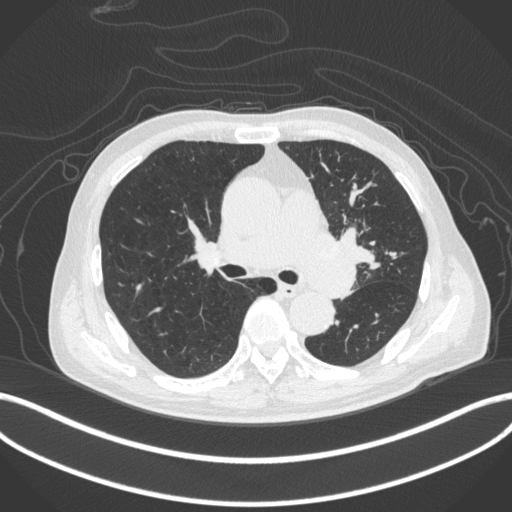
Chest CT, one axial slice. Position 263 of 420 along the scan axis. Lung window (W 1500 / L -600 HU). 1 mm slice thickness. 512 × 512 image matrix, field of view 400 × 400 mm. Patient: male, 77 years. From the clinical record (not read from this slice): clinical TNM (as recorded): T3 N1 M0.
Structures marked on this image (bounding box drawn by a radiologist):
- lung tumour (recorded histology: adenocarcinoma): bounding box (x1, y1, x2, y2) in pixels: (300, 228, 368, 296)